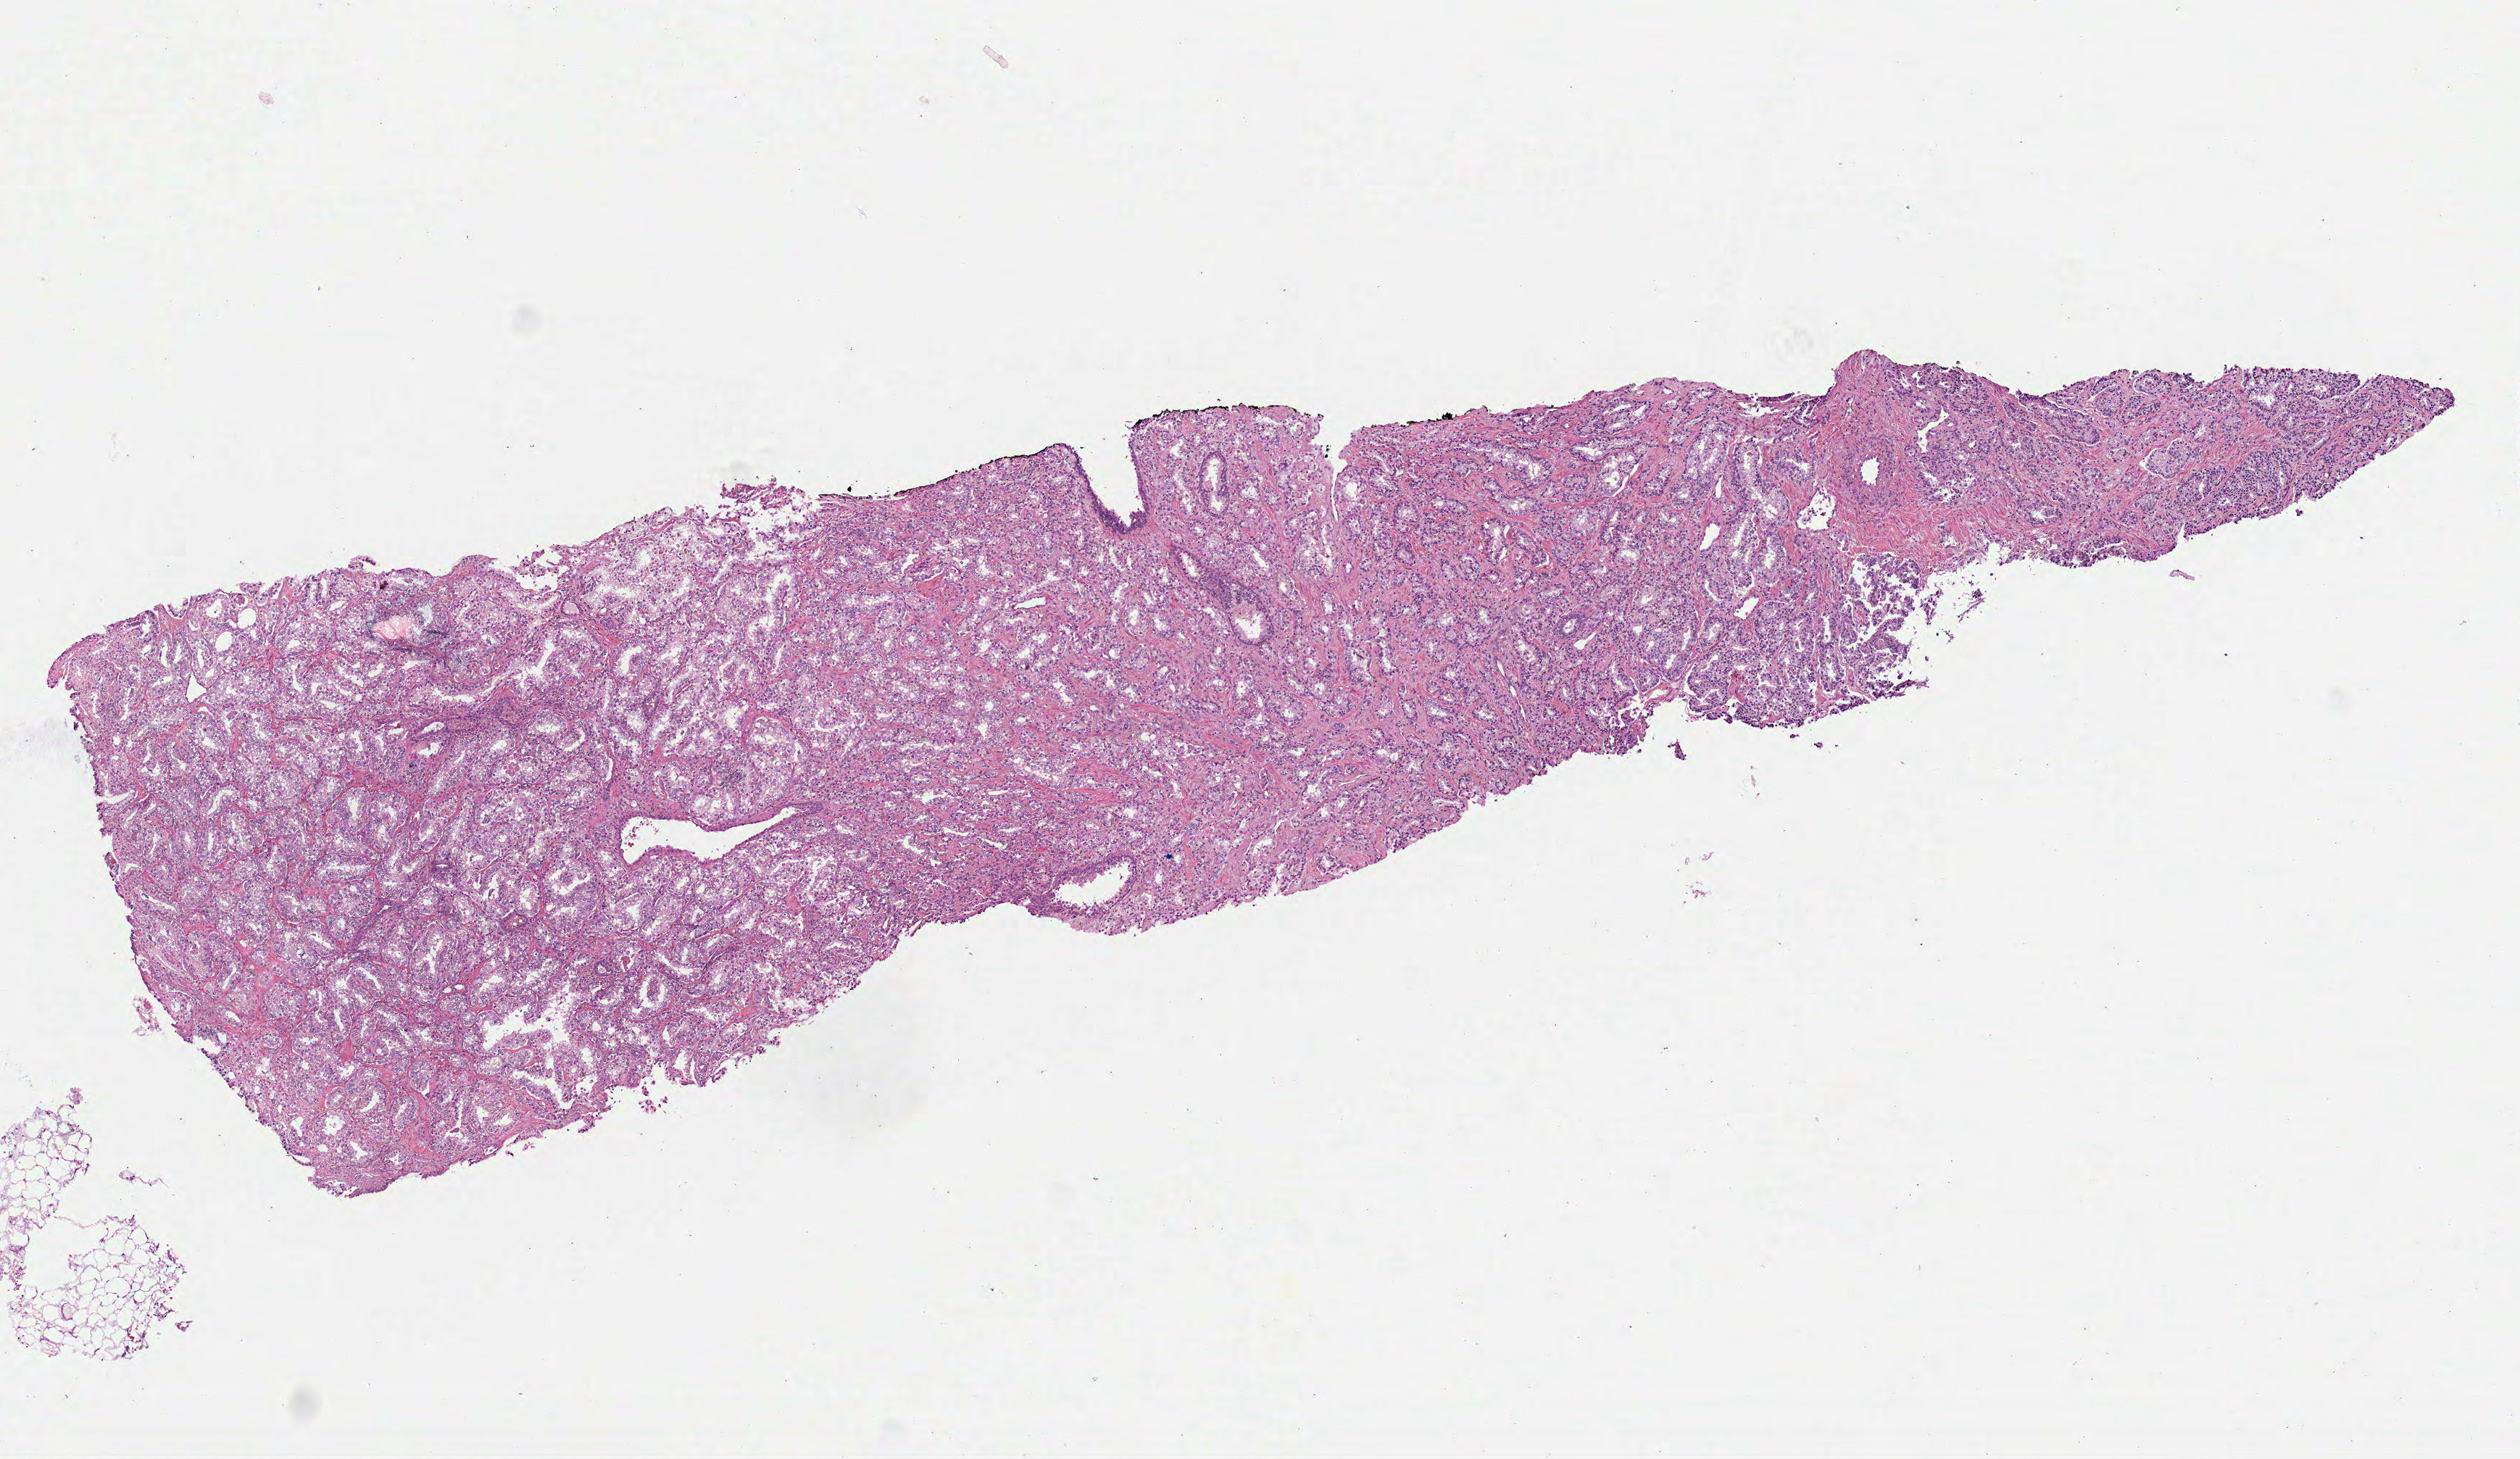
Digitized H&E-stained tissue section (whole slide), a low-resolution overview of the entire scanned area, about 7.0 x 4.1 mm (slide scanned at 40x). FFPE section. Primary tumour sample from the prostate. Male patient; age at initial diagnosis 69 years.
Diagnosis: Acinar cell carcinoma (prostate gland).